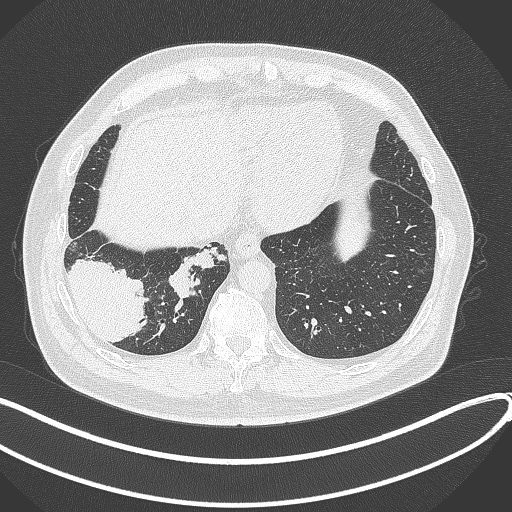
Chest CT, one axial slice; slice 79 of 360 in the series (ordered by position); reconstruction kernel B70f; lung window (W 1500 / L -600 HU); 1 mm slice thickness; 512 × 512 image matrix, field of view 400 × 400 mm. Patient: male, 59 years.
Structures marked on this image (bounding box drawn by a radiologist):
- lung tumour (recorded histology: adenocarcinoma): bounding box (x1, y1, x2, y2) in pixels: (63, 255, 151, 343)